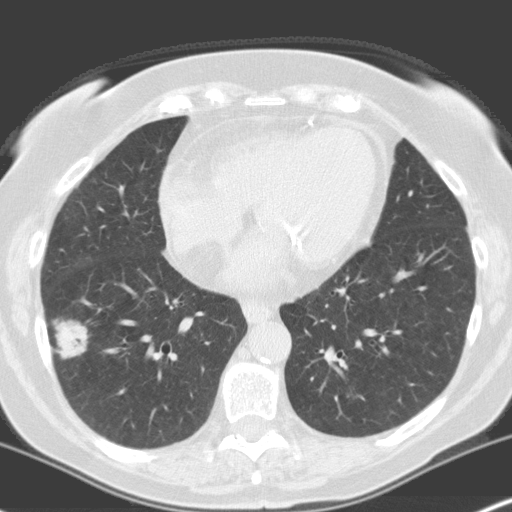
Chest CT (low-dose screening protocol), one axial image; first (baseline) screen; lung window (W 1500 / L -600 HU). Female, age 70 years at enrolment. Current smoker at enrolment.
Expert-annotated lung lesion, bounding box <34,306,100,375> (left, top, right, bottom; pixels). The screening reader recorded 4 non-calcified nodules or masses ≥4 mm on this exam; which of them this box marks is not recorded. Participant outcome: lung cancer diagnosed 28 days after this screen — adenocarcinoma, NOS, right lower lobe, moderately differentiated (G2), stage IV (AJCC 6th edition), 28 mm at pathology.